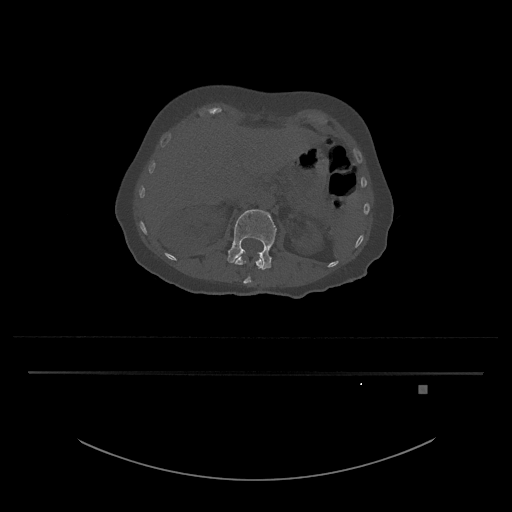
CT including the spine, one axial slice; position 513 of 797 along the scan axis; reconstruction kernel Br40s/3; bone window (W 1800 / L 400 HU); 512 × 512 image matrix, field of view 500 × 500 mm. Patient: female, 57 years. From the clinical record (not read from this slice): primary cancer: cervical.
Annotated regions visible in this slice (semi-automatically segmented with operator editing):
- L1 vertebra: box from (x=235, y=254) to (x=264, y=284) px